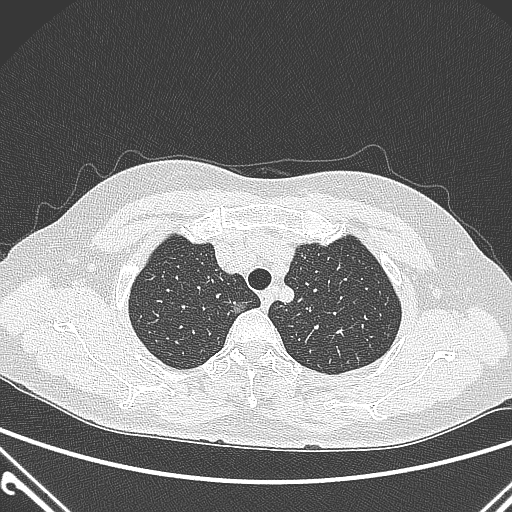
Chest CT, one axial slice; position 236 of 300 along the scan axis; lung window (W 1500 / L -600 HU); 1 mm slice thickness; 512 × 512 image matrix, field of view 350 × 350 mm. Patient: female, 54 years. From the clinical record (not read from this slice): clinical TNM (as recorded): T1a N0 M0.
Structures marked on this image (rectangle marked by the reading radiologist):
- lung tumour (recorded histology: adenocarcinoma): bounding box <226,296,254,324> (left, top, right, bottom; pixels)